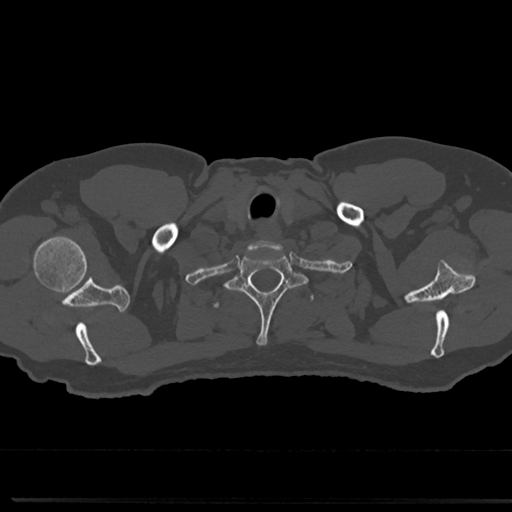
CT including the spine, one axial slice. Slice 674 of 817 in the series (ordered by position). Reconstruction kernel Br40s/3. 120 kVp. Bone window (W 1800 / L 400 HU). 0.5 mm slice thickness. 512 × 512 image matrix, field of view 355 × 355 mm. Patient: male, 61 years. From the clinical record (not read from this slice): primary cancer: prostate.
Structures marked on this image (semi-automatically segmented with operator editing):
- T1 vertebra: bounding box (x1, y1, x2, y2) in pixels: (232, 249, 301, 346)
- T2 vertebra: (212, 291, 315, 314)